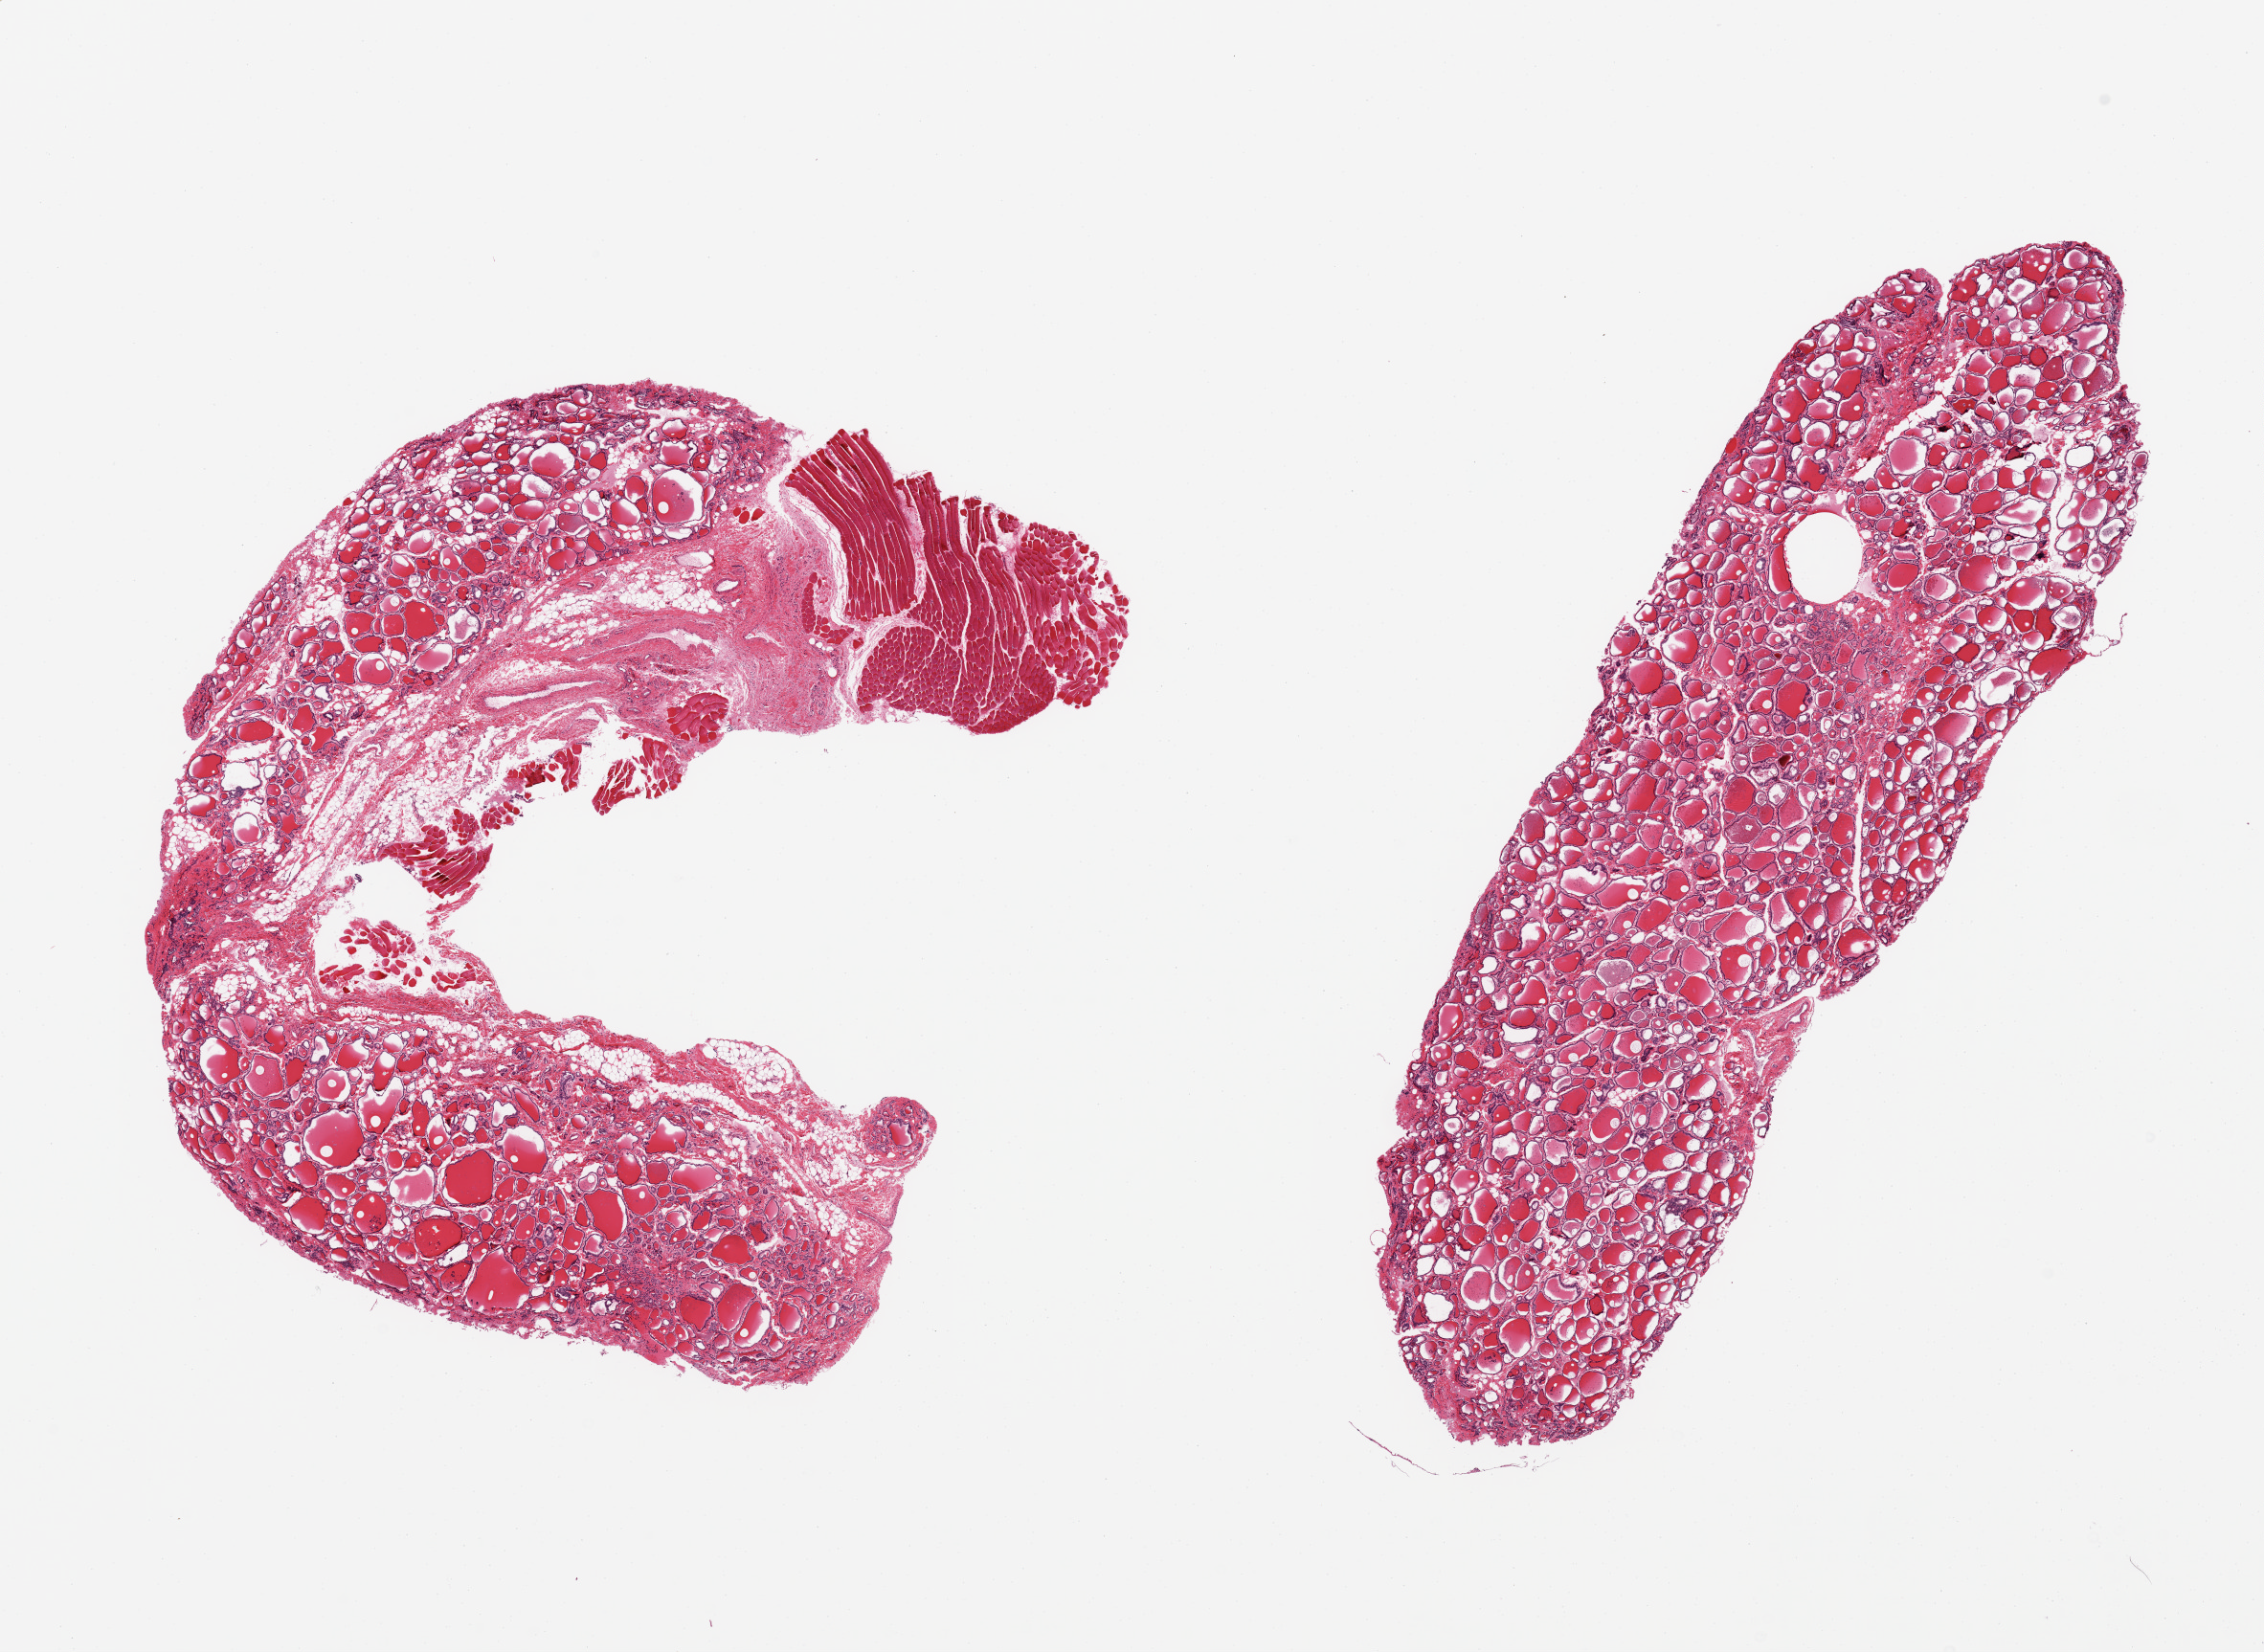
H&E whole-slide image — low-resolution overview of the scanned area, about 18.7 x 13.7 mm. PAXgene-fixed, paraffin-embedded tissue. Sampled site (target tissue): thyroid. Tissue donor sample. Donor sex: male.
* review note (as recorded): 2 pieces; 1 with up to 2.3mm adherent skeletal muscle